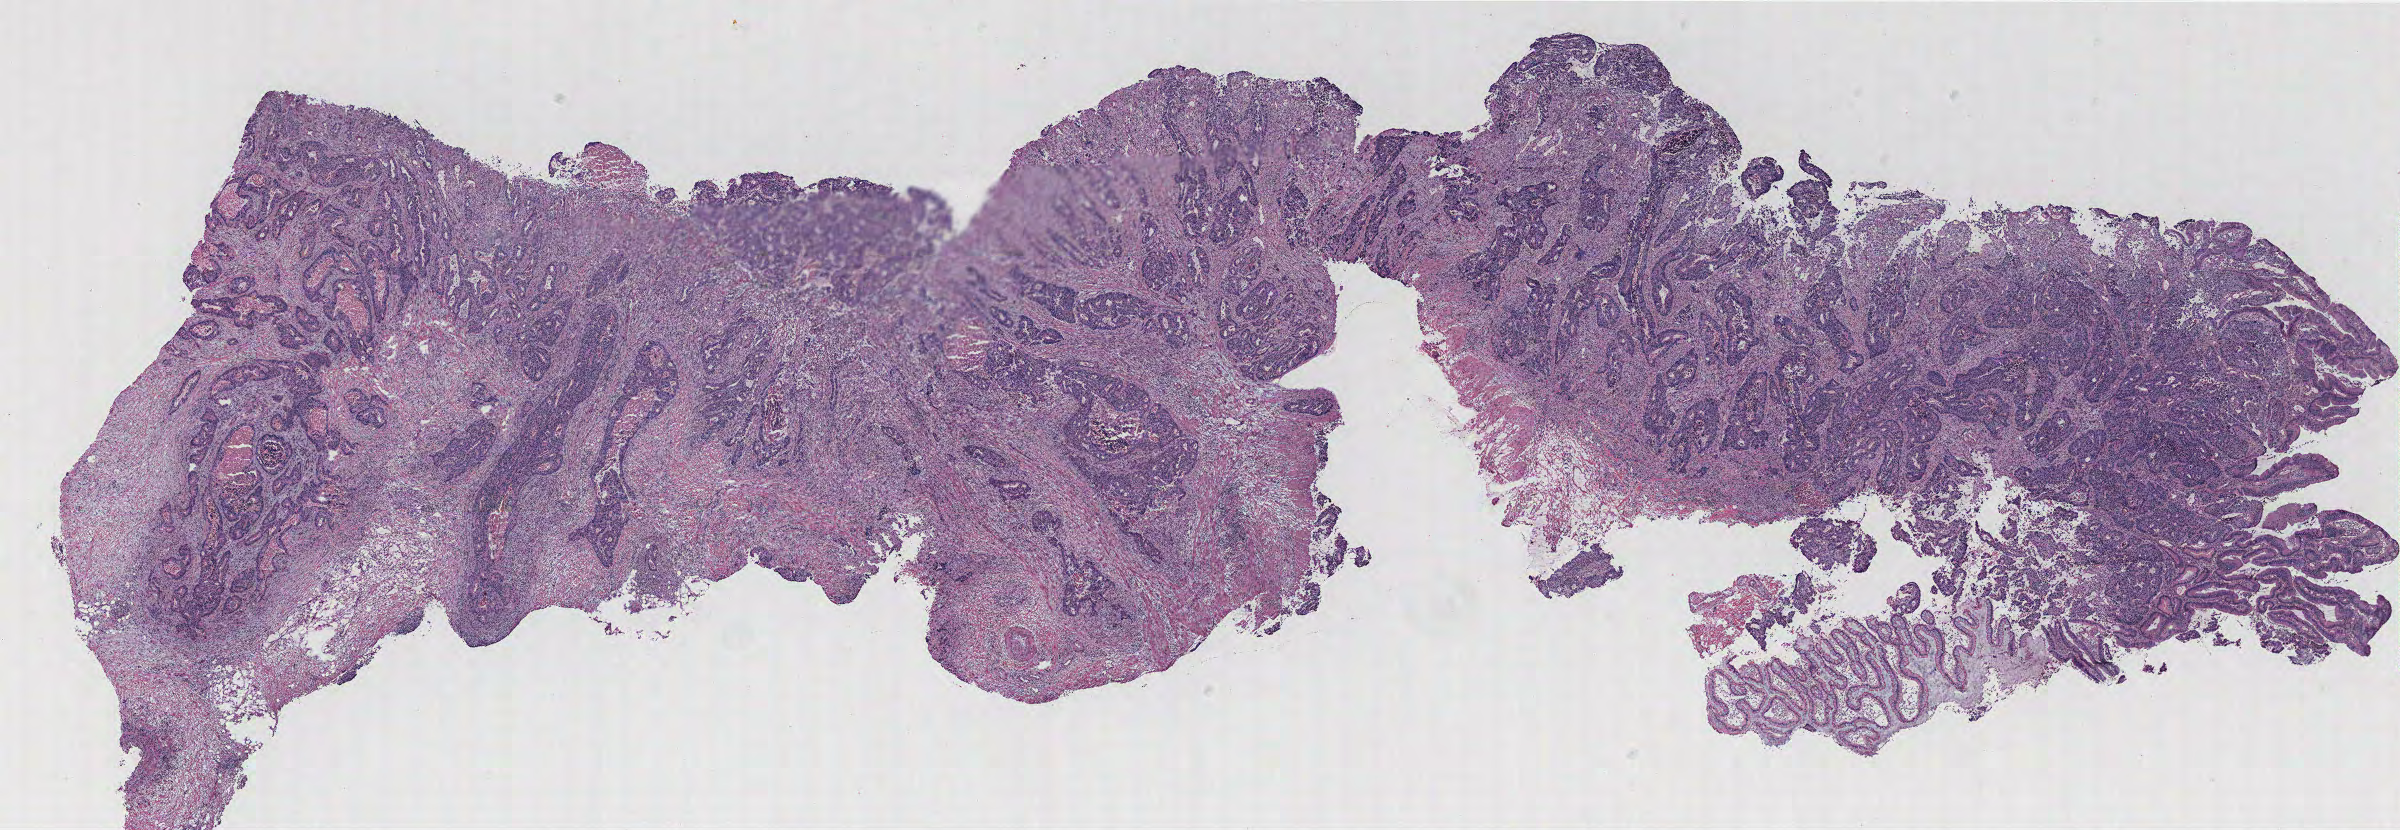
Whole-slide histology image, Hematoxylin and eosin (H&E) stained — whole scanned area (about 19.2 x 6.6 mm, from a 40x scan) shown as a low-resolution overview; colon, tissue type not recorded.
Patient diagnosis (cohort enrolment): colon cancer (colon).